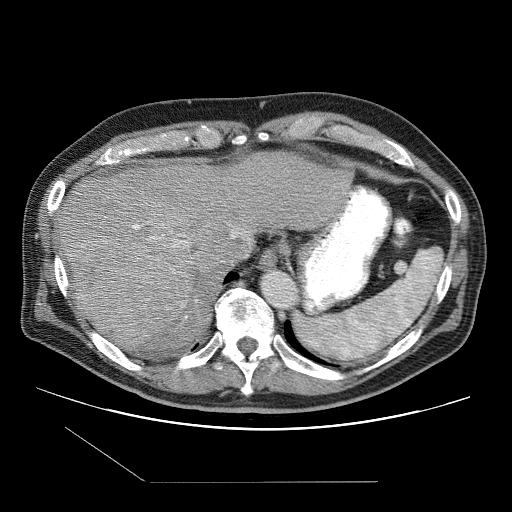
Contrast-enhanced abdominal CT (liver protocol), one axial slice. Position 81 of 109 along the scan axis. Reconstruction kernel STANDARD. One of 2 acquisitions stored at this slice position. Soft-tissue window (W 400 / L 40 HU). 2.5 mm slice thickness. 512 × 512 image matrix, field of view 400 × 400 mm. Case-level facts recorded for this patient, not image findings: diagnosis: hepatocellular carcinoma (patient treated with transarterial chemoembolisation; whether this scan precedes or follows treatment is not stated here); TNM stage (as recorded): Stage-IIIB; Child-Pugh class: A; tumour differentiation: well differentiated.
Structures marked on this image (semi-automatically segmented with operator editing):
- liver parenchyma outside the tumour (the mass and vessels are separate outlines, so this box may not span the whole liver): bounding box (x1, y1, x2, y2) in pixels: (58, 151, 350, 352)
- mass: (66, 237, 197, 345)
- liver vessels: (132, 224, 248, 318)